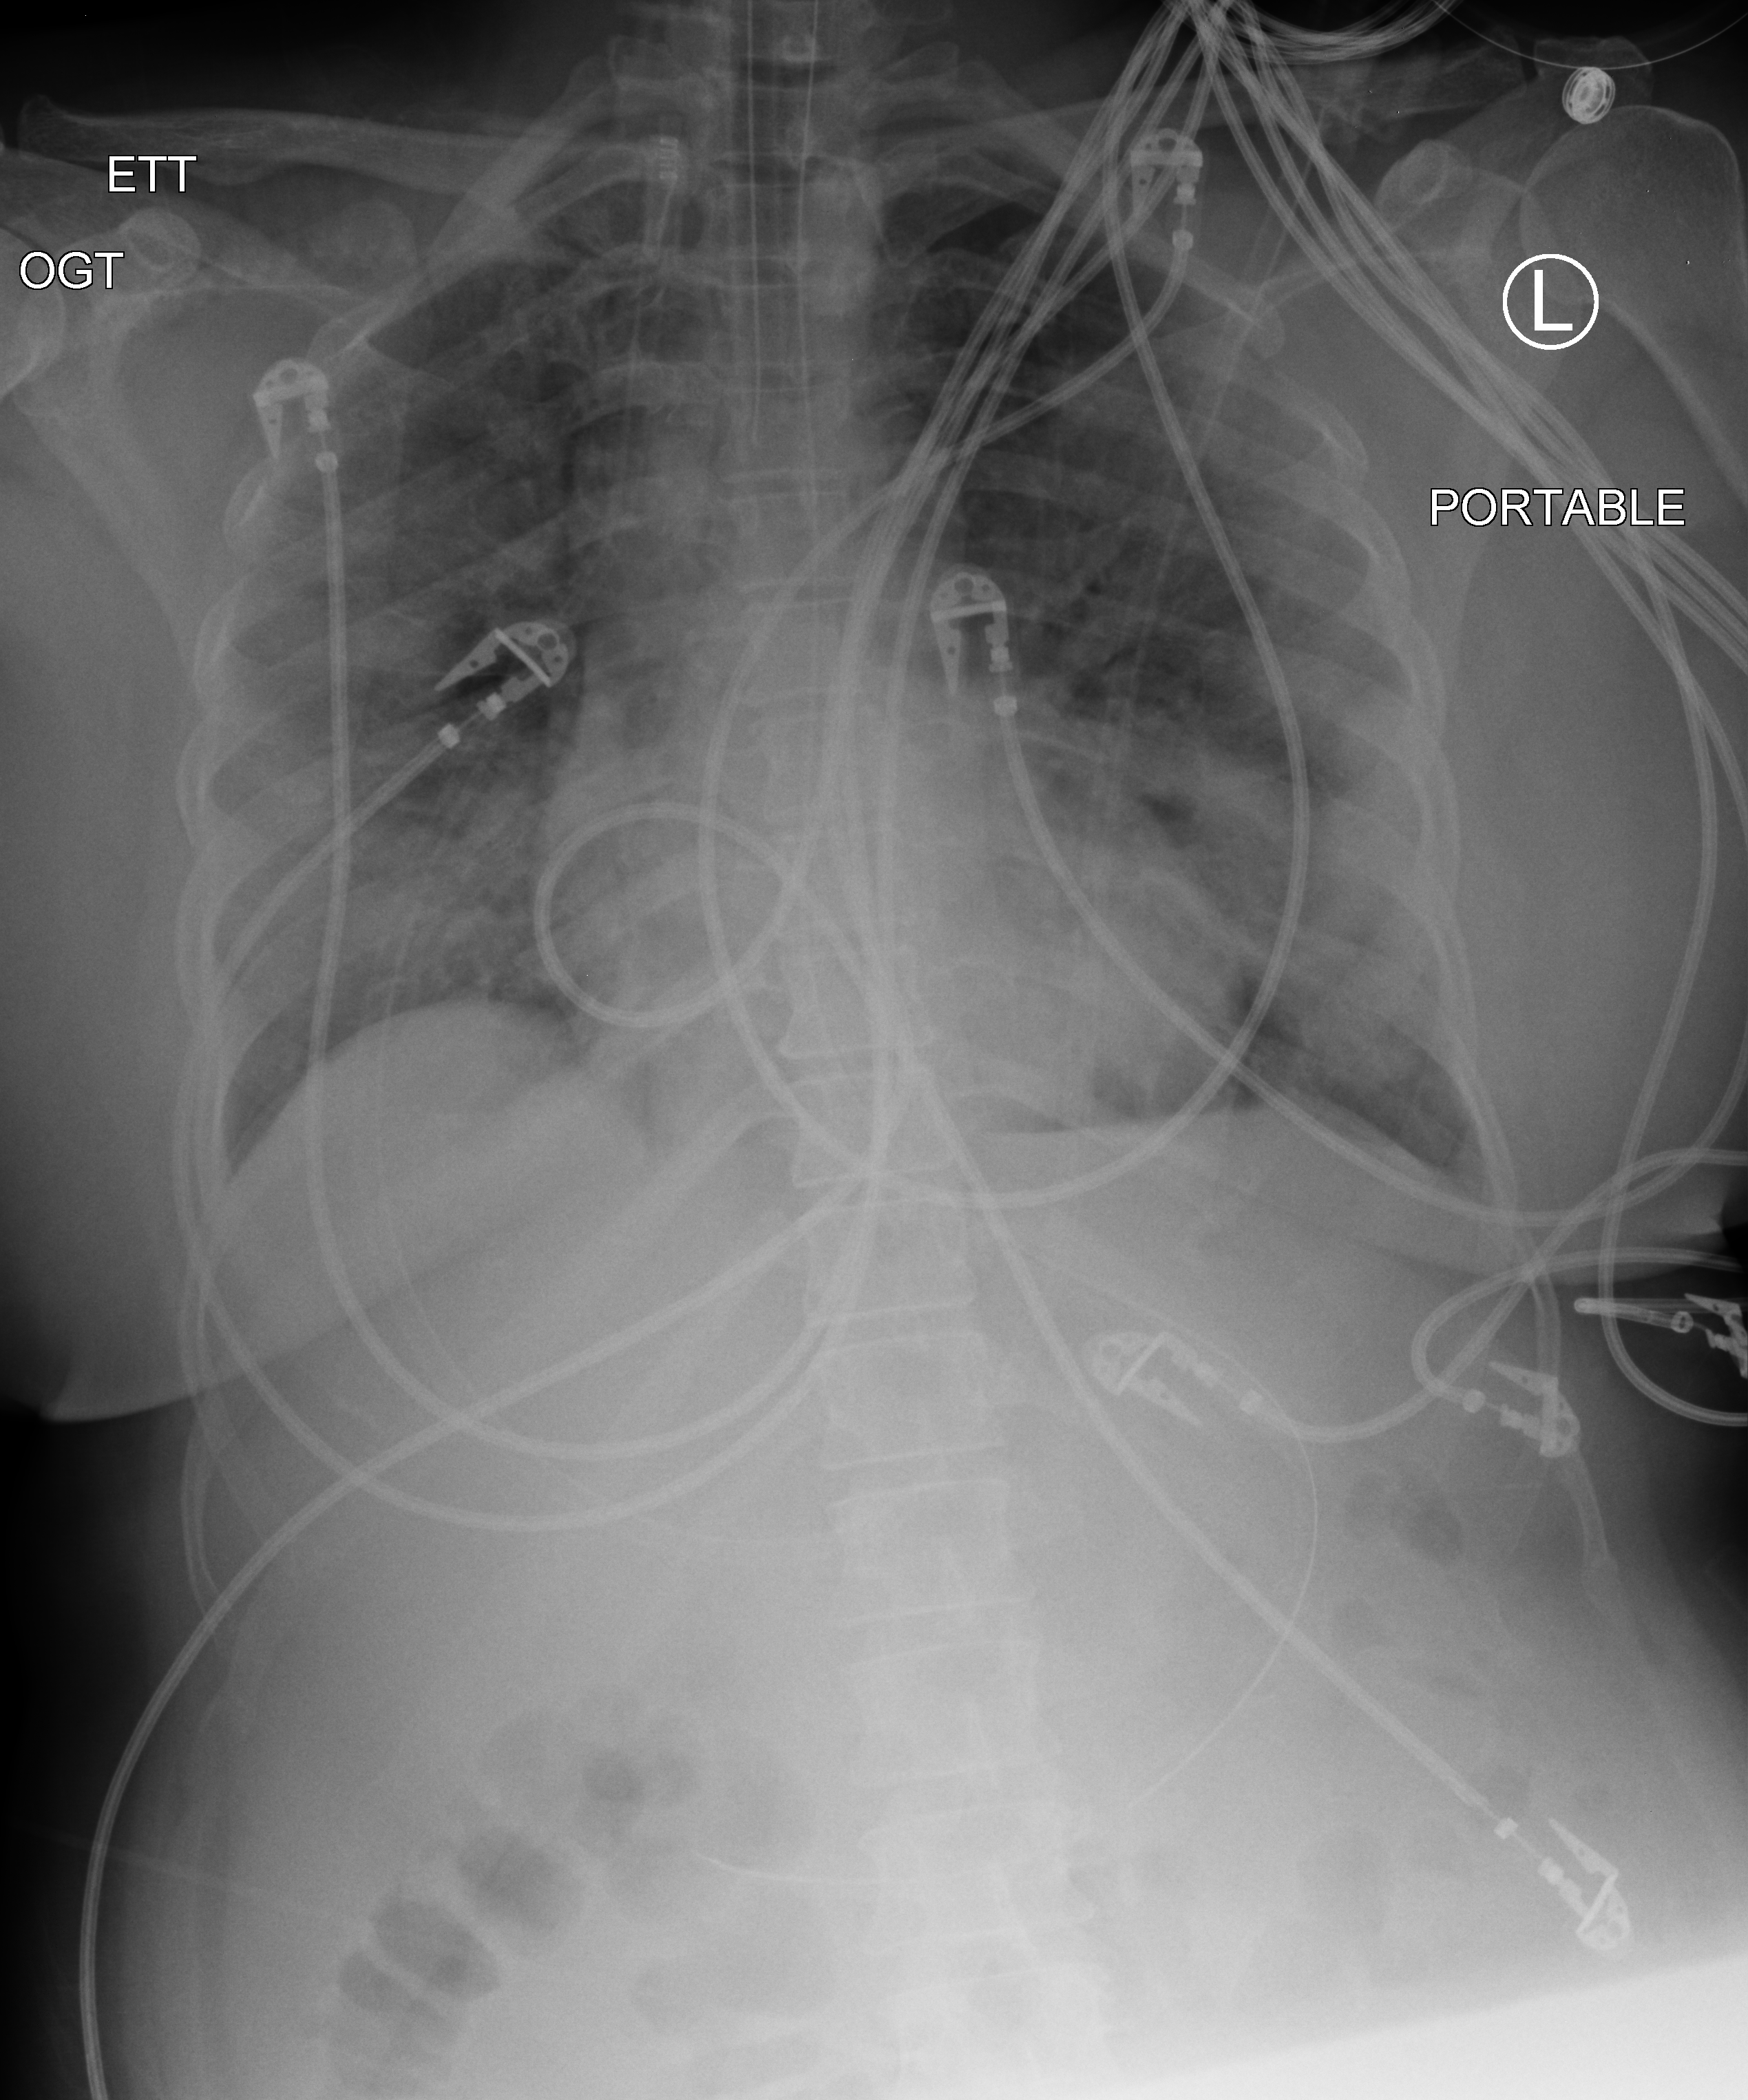
Portable chest radiograph, anteroposterior (AP) projection. Patient hospitalised with COVID-19; male, aged 18–59 years.
Hospital-stay facts (about this admission, not read from this image; timing relative to this image not recorded):
- admitted to intensive care during this hospital stay: yes
- COPD (admission record): no